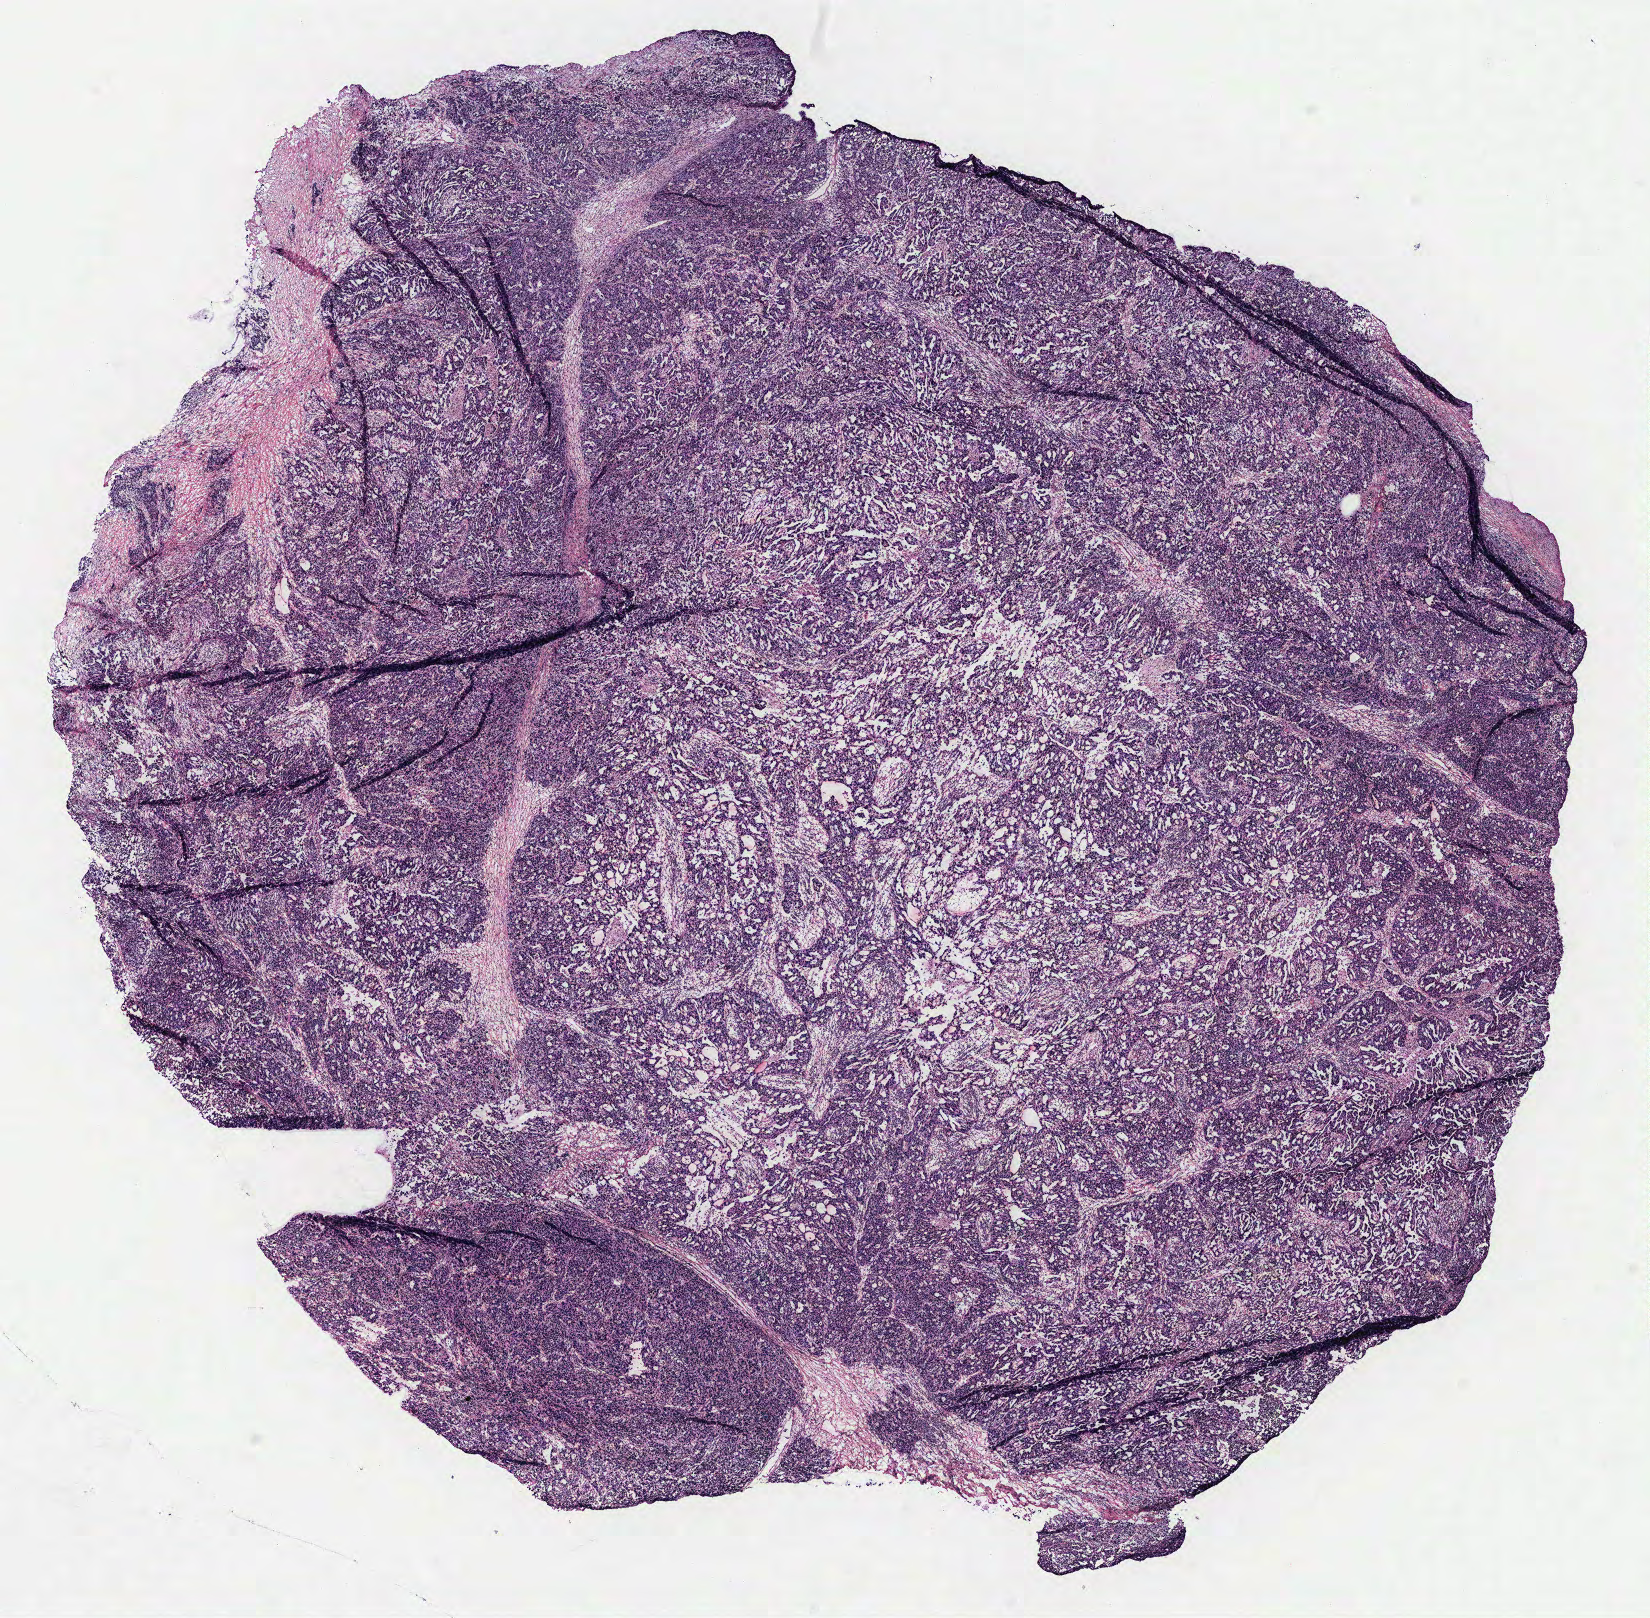
Digitized H&E-stained tissue section (whole slide), low-resolution overview of the scanned area, about 13.2 x 12.9 mm; tumour tissue sample, ovary. 52-year-old female patient.
• primary tumour site (as recorded): fallopian tube
• histologic diagnosis: Serous adenocarcinoma, NOS